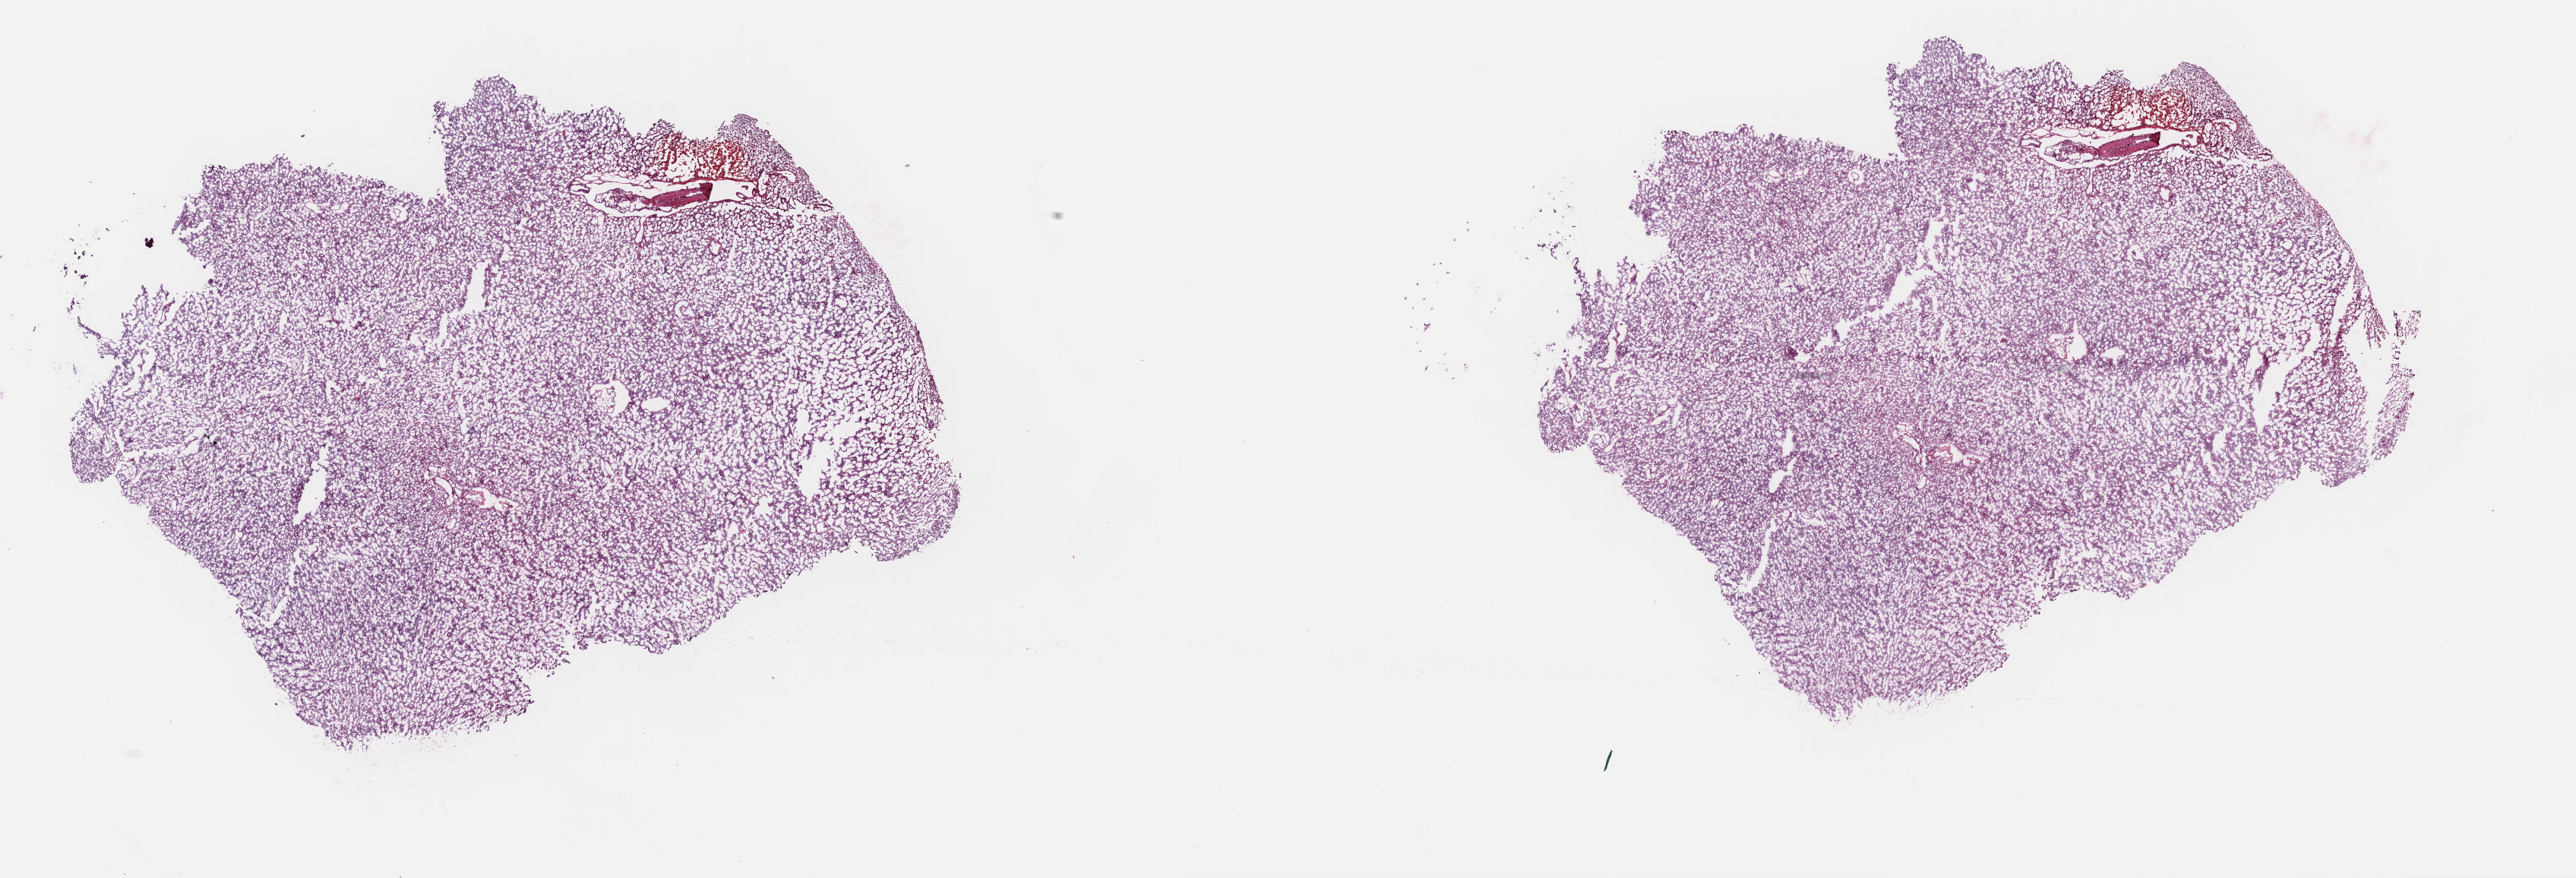
H&E whole-slide image — low-resolution overview of the scanned area, about 26.8 x 9.1 mm; frozen section from the top of the tissue portion; primary tumour sample from the brain. Male patient; age at initial diagnosis 52 years. Histologic grade: G3 (poorly differentiated). Slide review estimates, as recorded: tumour cells 60%, tumour nuclei 85%, normal cells 10%, stromal cells 30%, necrosis 0%. Infiltration values recorded for this section: lymphocyte infiltration 0%, monocyte infiltration 0%, neutrophil infiltration 0%.
- pathologic diagnosis: Oligodendroglioma, anaplastic (cerebrum)